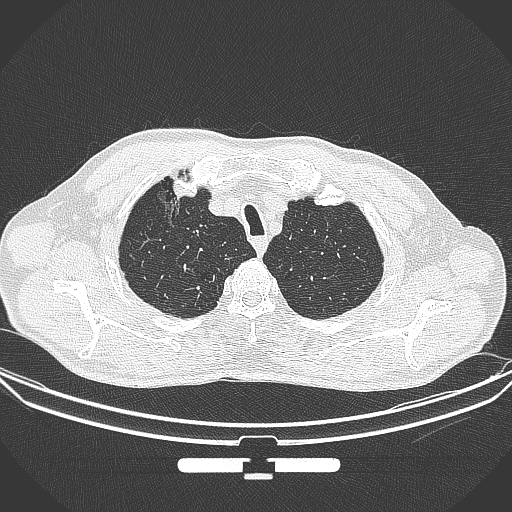
Chest CT, one axial slice; position 296 of 355 along the scan axis; 120 kVp; lung window (W 1500 / L -600 HU); 1 mm slice thickness; 512 × 512 image matrix, field of view 399 × 399 mm. Patient: male, 67 years. From the clinical record (not read from this slice): clinical TNM (as recorded): T1c N0 M0; histopathological grade: G2.
Outlined on this slice (rectangle marked by the reading radiologist):
- lung tumour (recorded histology: adenocarcinoma): bounding box <151,184,187,230> (left, top, right, bottom; pixels)